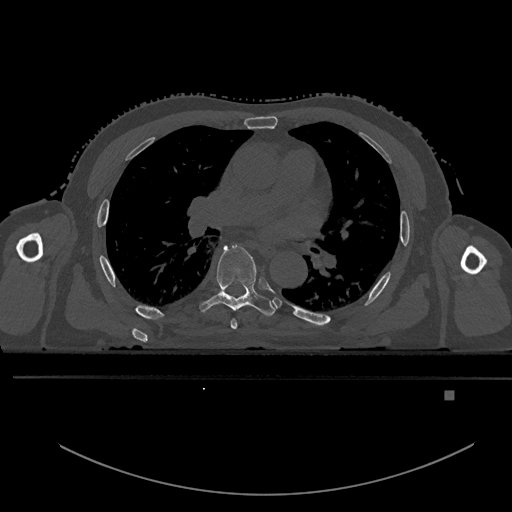
CT including the spine, one axial slice. Slice 313 of 969 in the series (ordered by position). Bone window (W 1800 / L 400 HU). 512 × 512 image matrix, field of view 456 × 456 mm. Patient: male, 82 years. From the clinical record (not read from this slice): primary cancer: prostate.
Outlined on this slice (semi-automatic segmentation, software-assisted and operator-edited):
- T5 vertebra: bounding box <230,319,237,330> (left, top, right, bottom; pixels)
- T6 vertebra: <199,244,277,317>